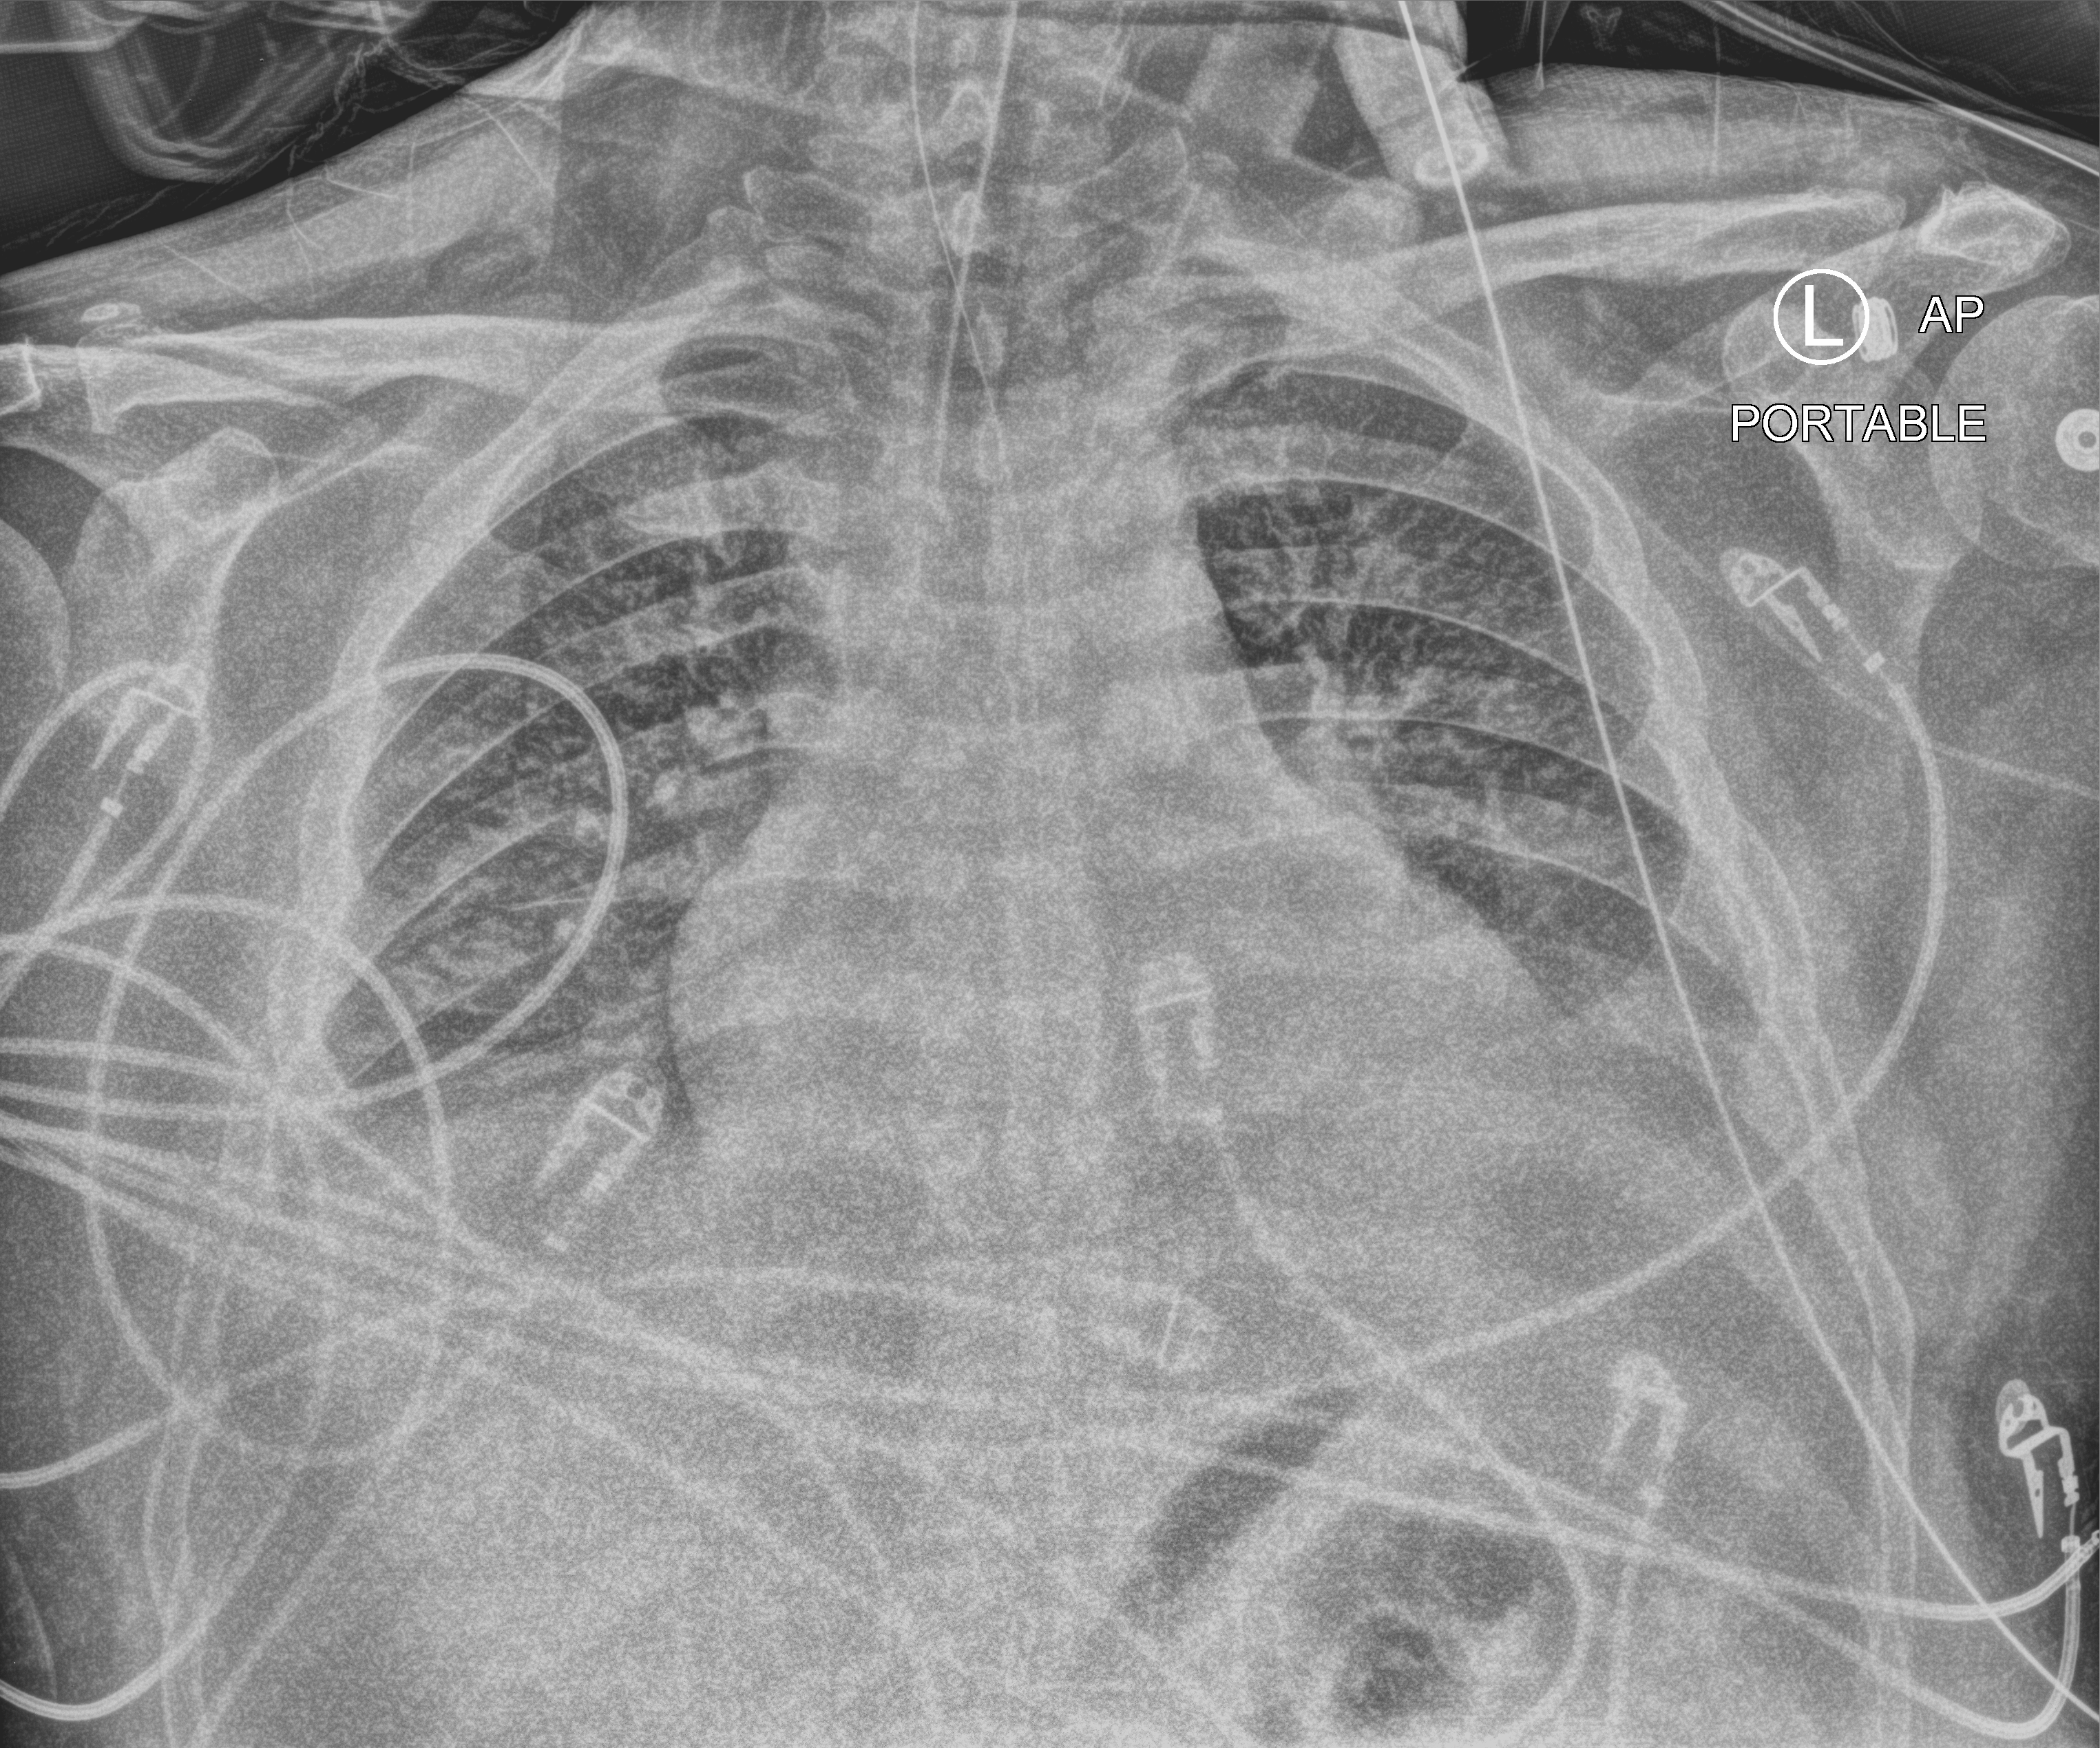
Chest X-ray (portable); anteroposterior (AP) projection. Patient hospitalised with COVID-19; male, aged 18–59 years.
Hospital-stay facts (about this admission, not read from this image; timing relative to this image not recorded): length of hospital stay: 65 days; admitted to intensive care during this hospital stay: yes.